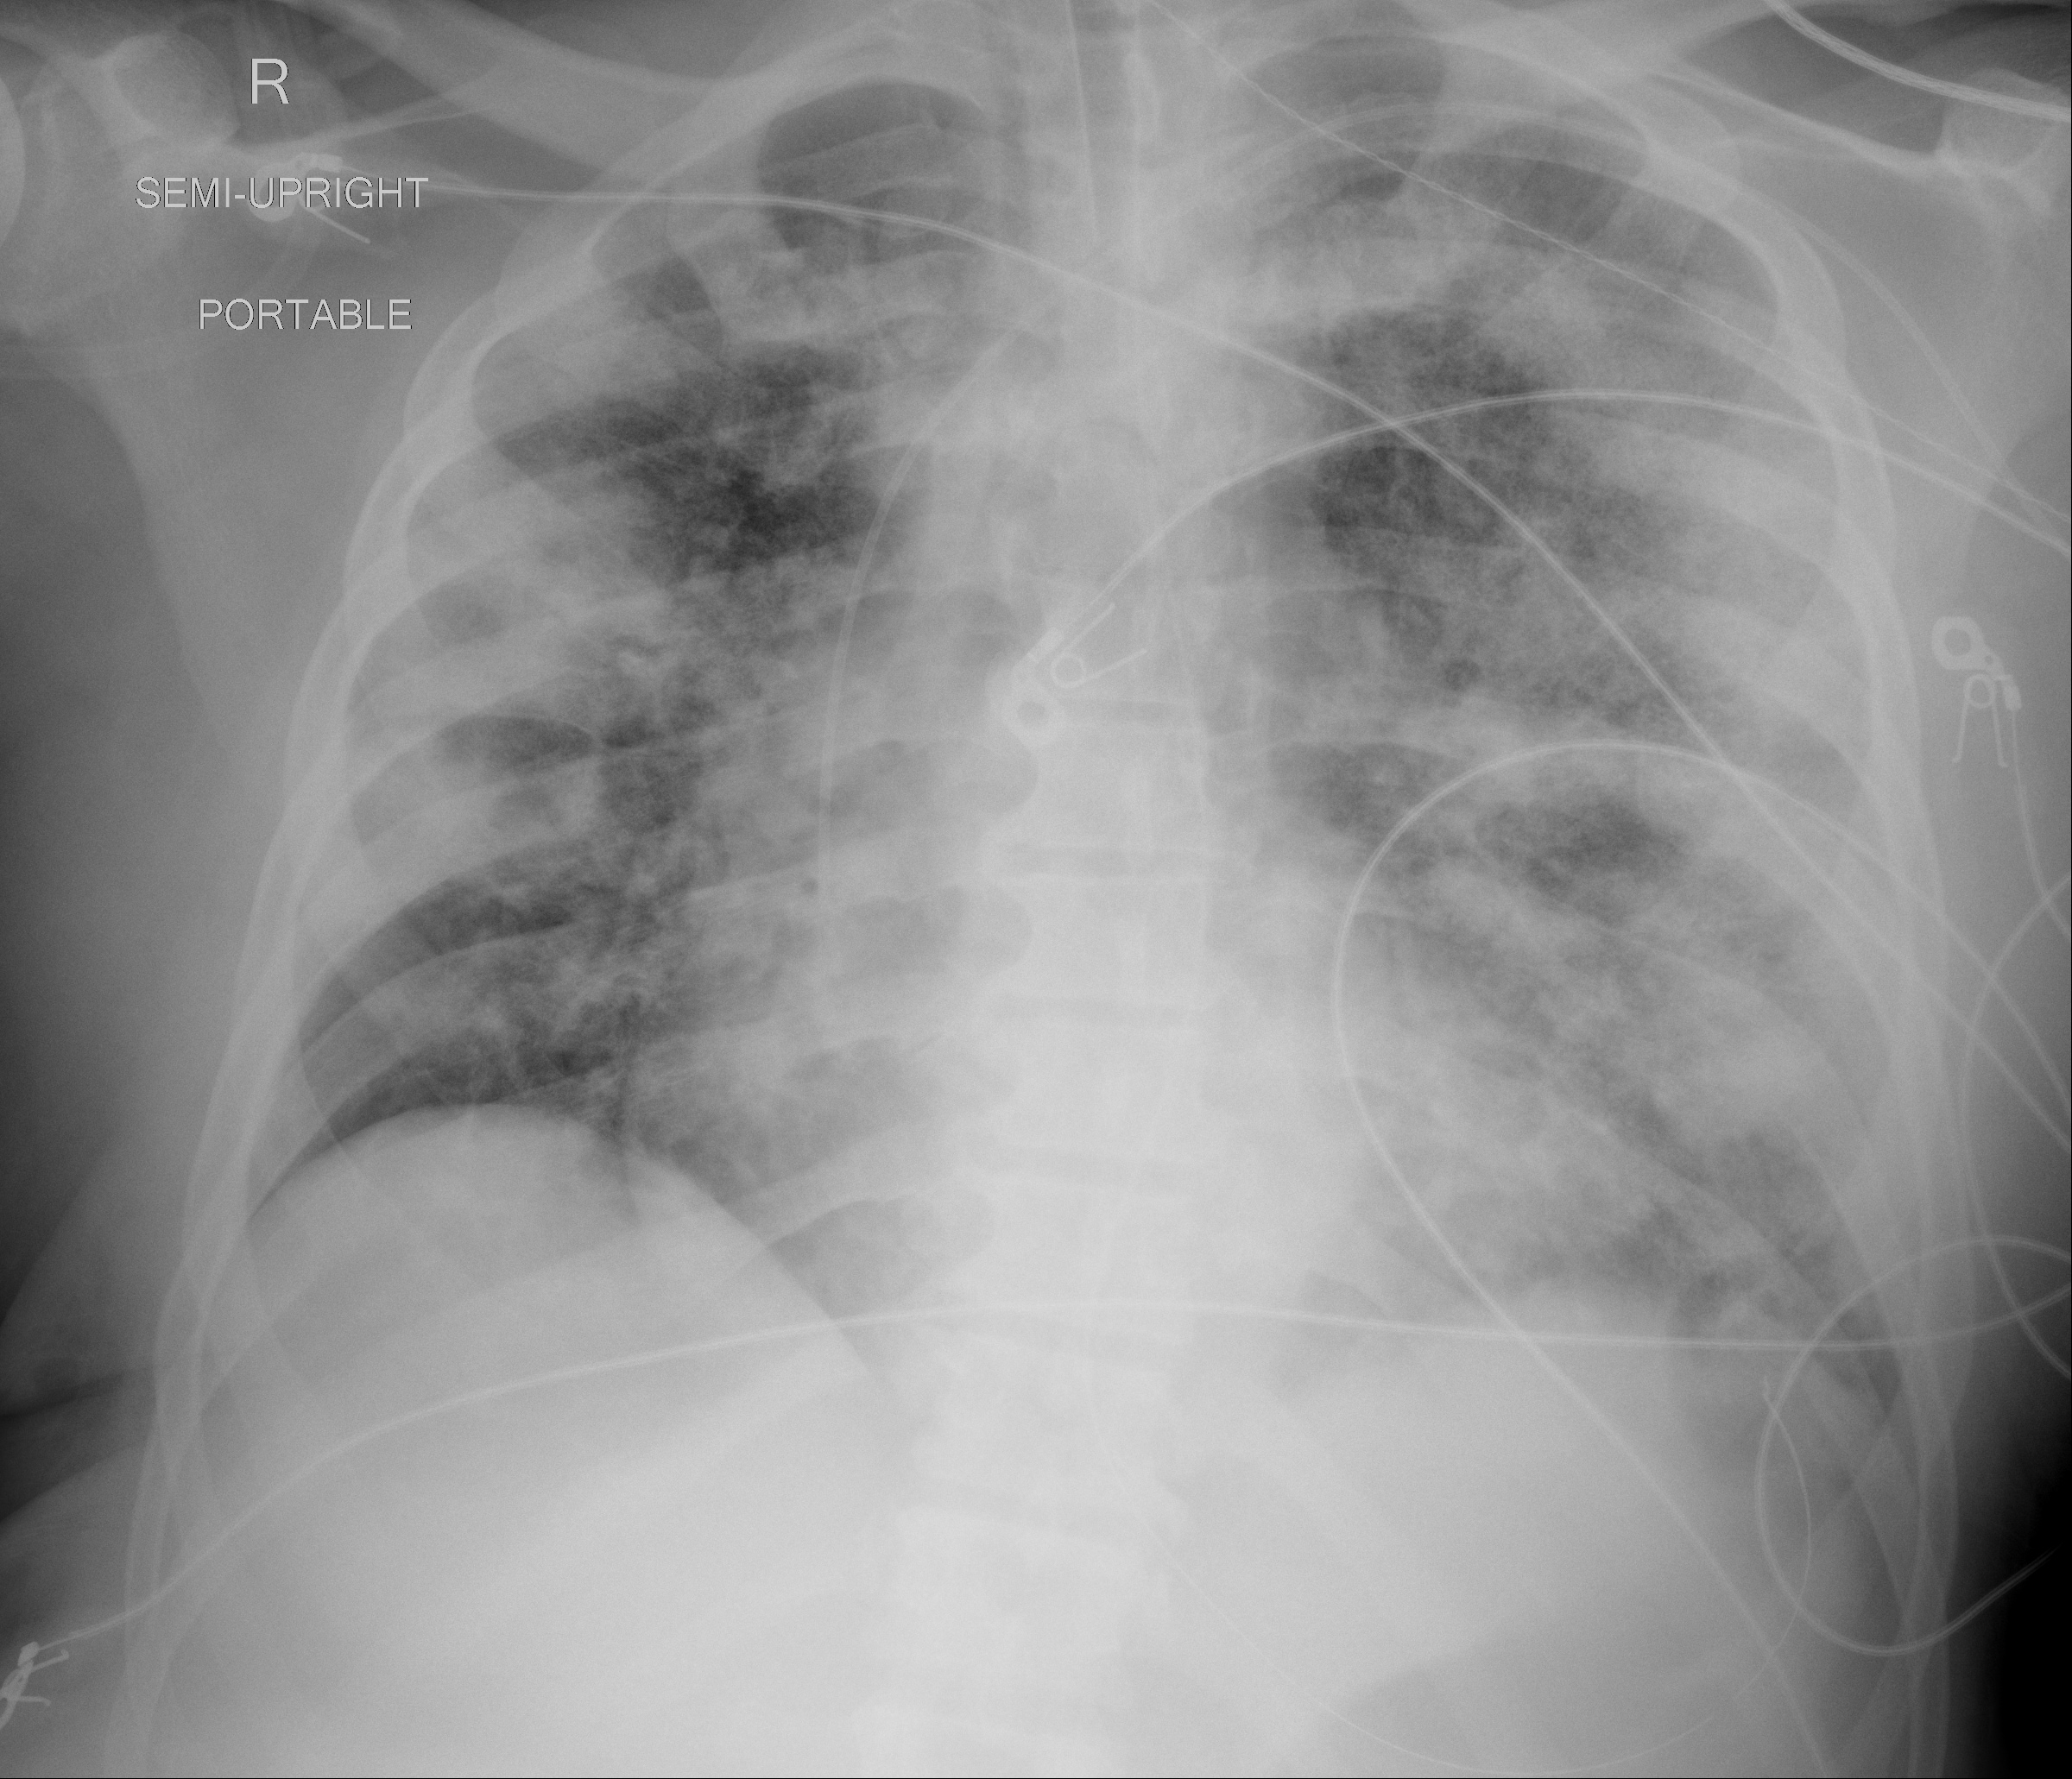
Portable chest radiograph, AP projection. Male patient, age 64 years; imaged 4 days after the COVID-19 diagnosis.
Radiologist key findings (as recorded): Significant worsening in multifocal infection involving both lung.